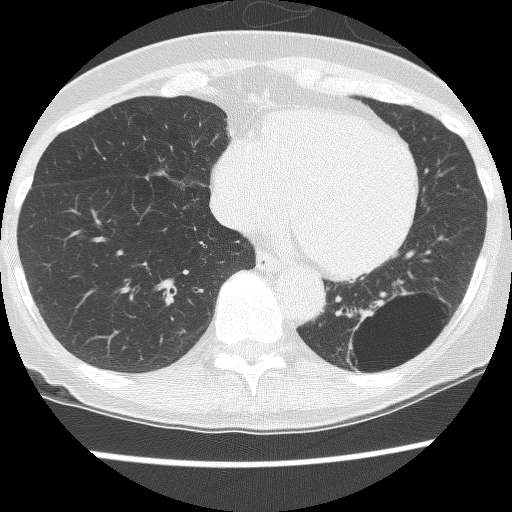
Axial slice from a low-dose chest CT screening exam, third annual screen, lung window (W 1500 / L -600 HU), 2.5 mm slice thickness, lung (sharp) reconstruction kernel (BONE), 120 kVp, slice 90 of 130 in the series. Female participant, aged 61 years at enrolment.
Expert reader's lesion annotation, box from (x=332, y=292) to (x=446, y=389) px. The screening reader recorded 2 non-calcified nodules or masses ≥4 mm on this exam (left lower lobe, left lower lobe); which of them this box marks is not recorded. Official screen result: positive, no significant change: stable abnormalities potentially related to lung cancer, unchanged since the prior screening exam. Participant outcome: lung cancer diagnosed 166 days after this screen — non-small cell carcinoma, left lower lobe, poorly differentiated (G3), stage IB (AJCC 6th edition), 100 mm at pathology.